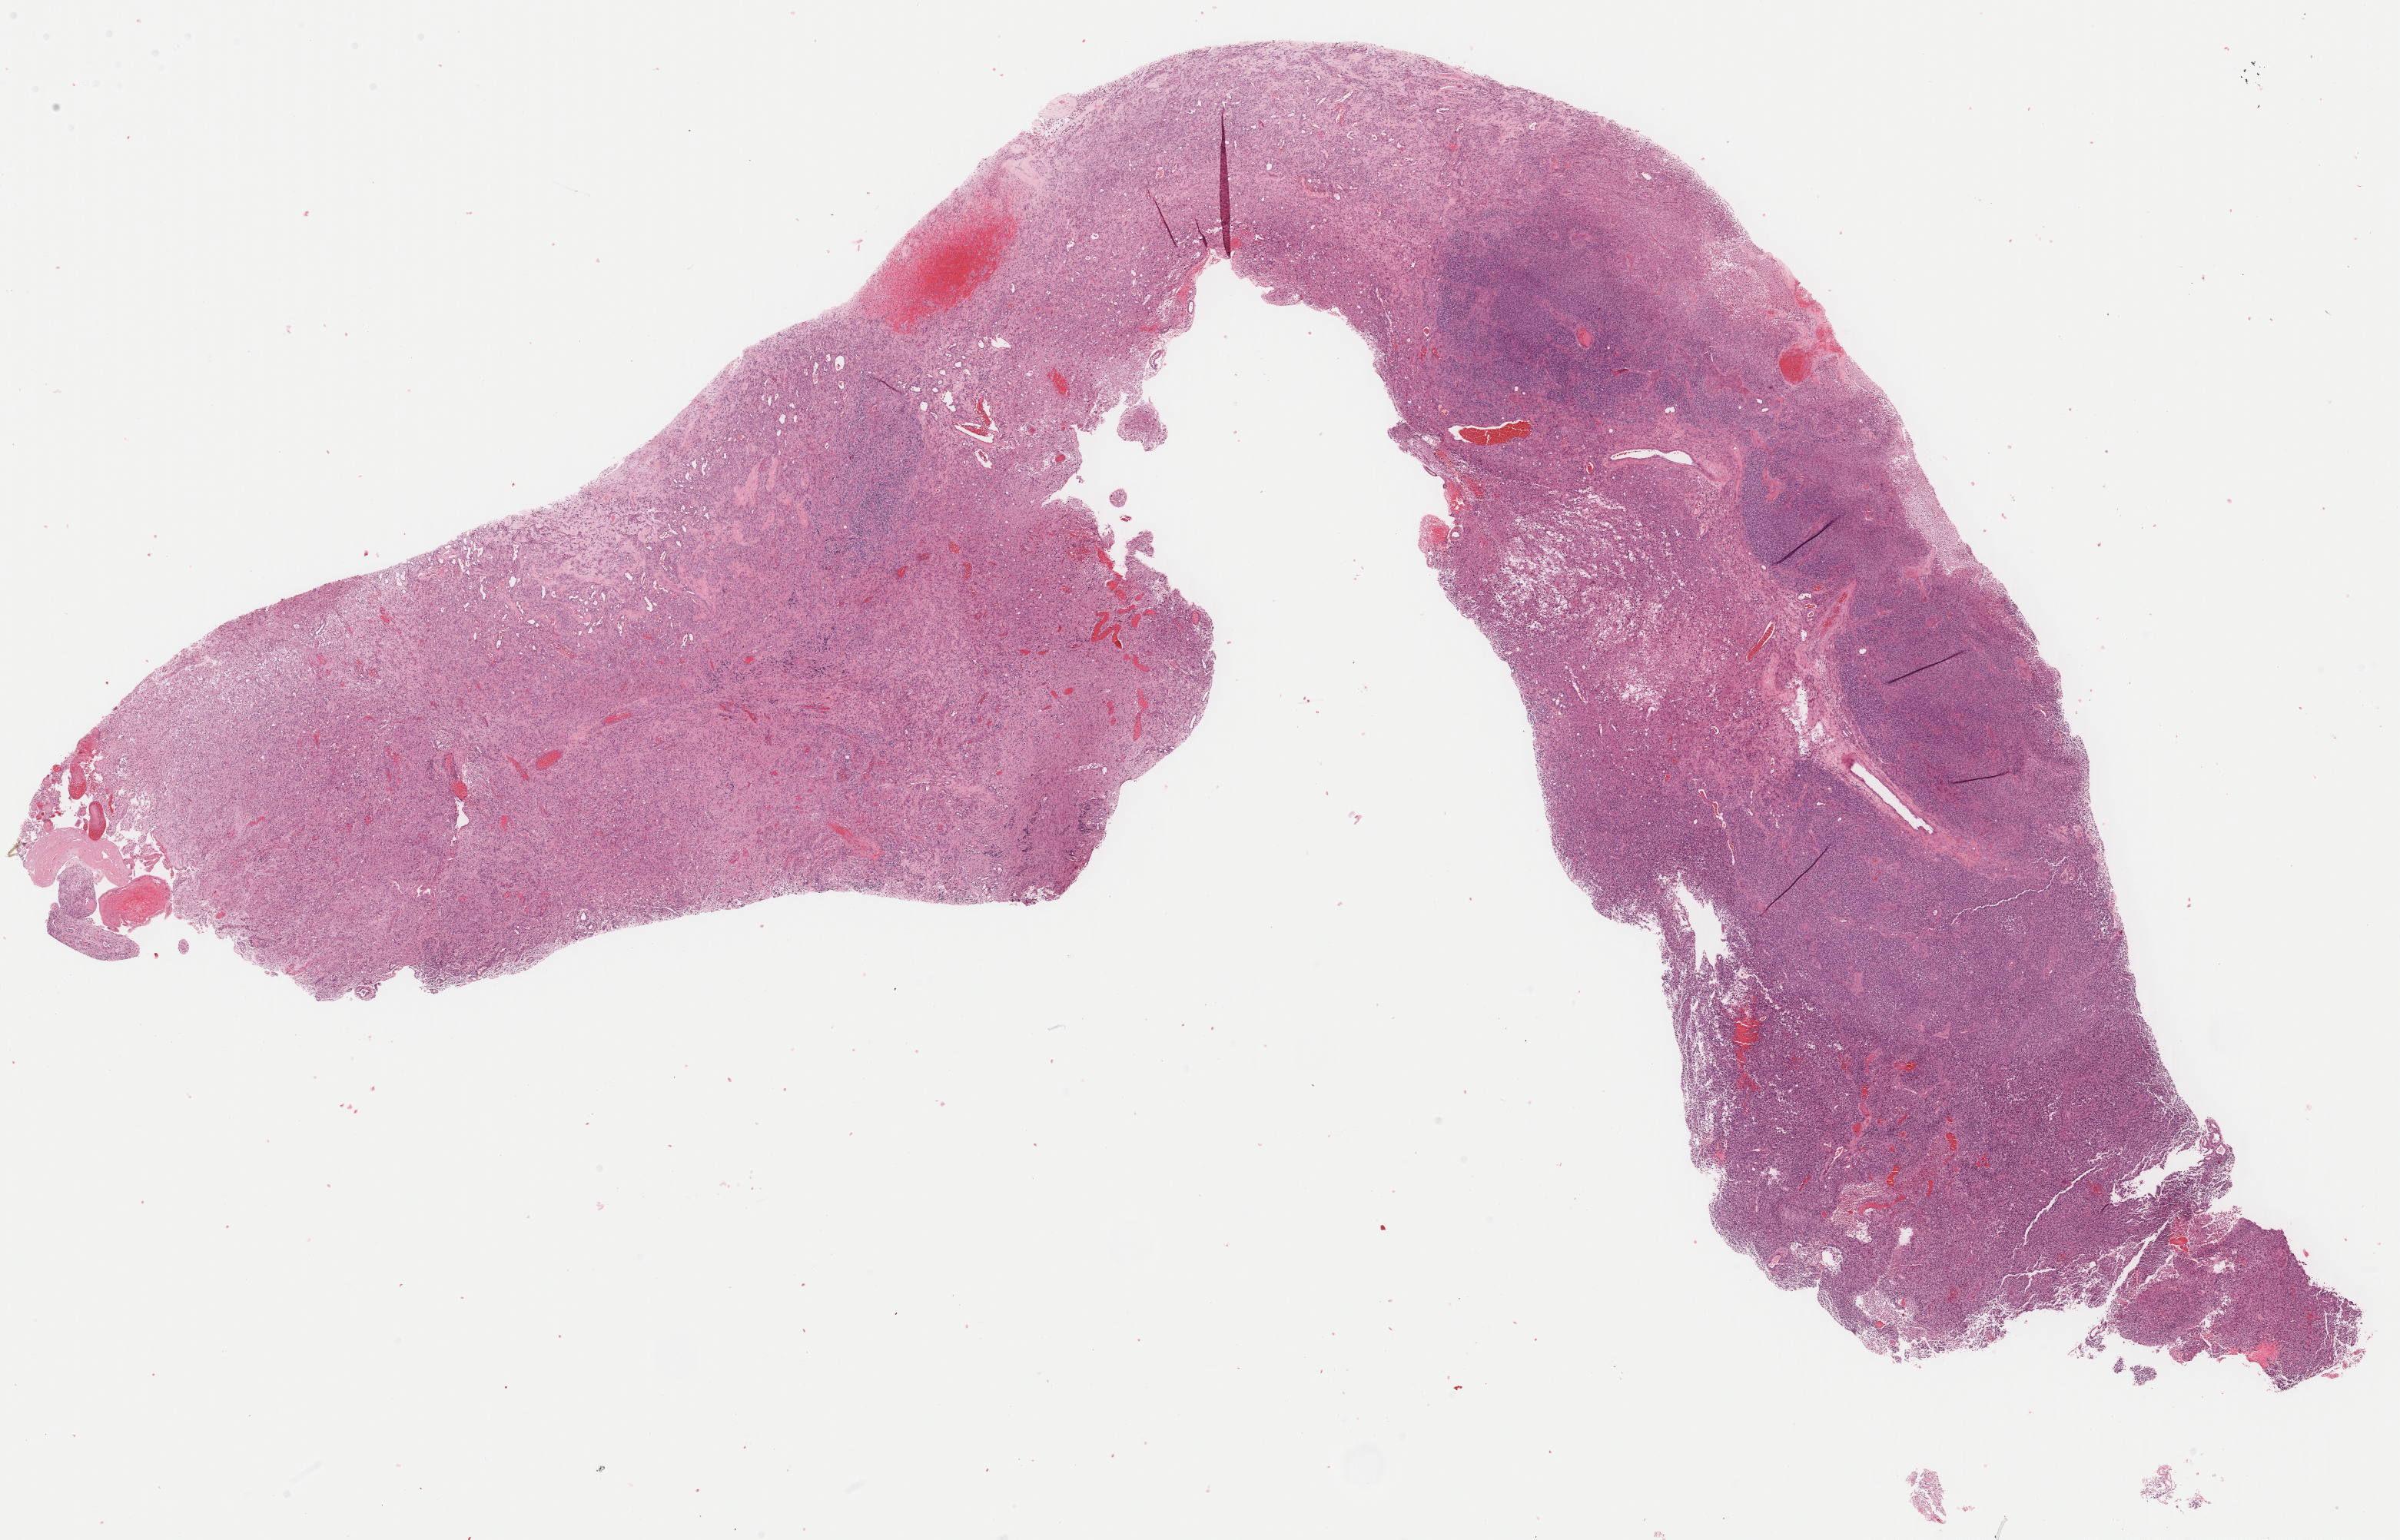
Digitized H&E-stained tissue section (whole slide) — shown as a low-resolution overview of the whole scanned area (about 24.6 x 15.8 mm, slide scanned at 40x); formalin-fixed paraffin-embedded (FFPE) diagnostic section; brain, primary tumour sample. Male patient; age at initial diagnosis 65 years.
- diagnosis: Glioblastoma